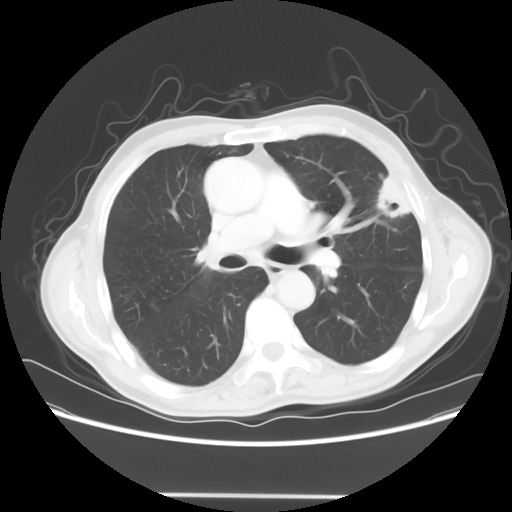
Chest CT, one axial slice. Slice 38 of 64 in the series (ordered by position). Reconstruction kernel STANDARD. Lung window (W 1500 / L -600 HU). 5 mm slice thickness. 512 × 512 image matrix, field of view 392 × 392 mm. Patient: male, 71 years. From the clinical record (not read from this slice): clinical TNM (as recorded): T1c N0 M0.
Structures marked on this image (bounding box drawn by a radiologist):
- lung tumour (recorded histology: adenocarcinoma): bounding box [x1, y1, x2, y2] px = [362, 167, 420, 230]